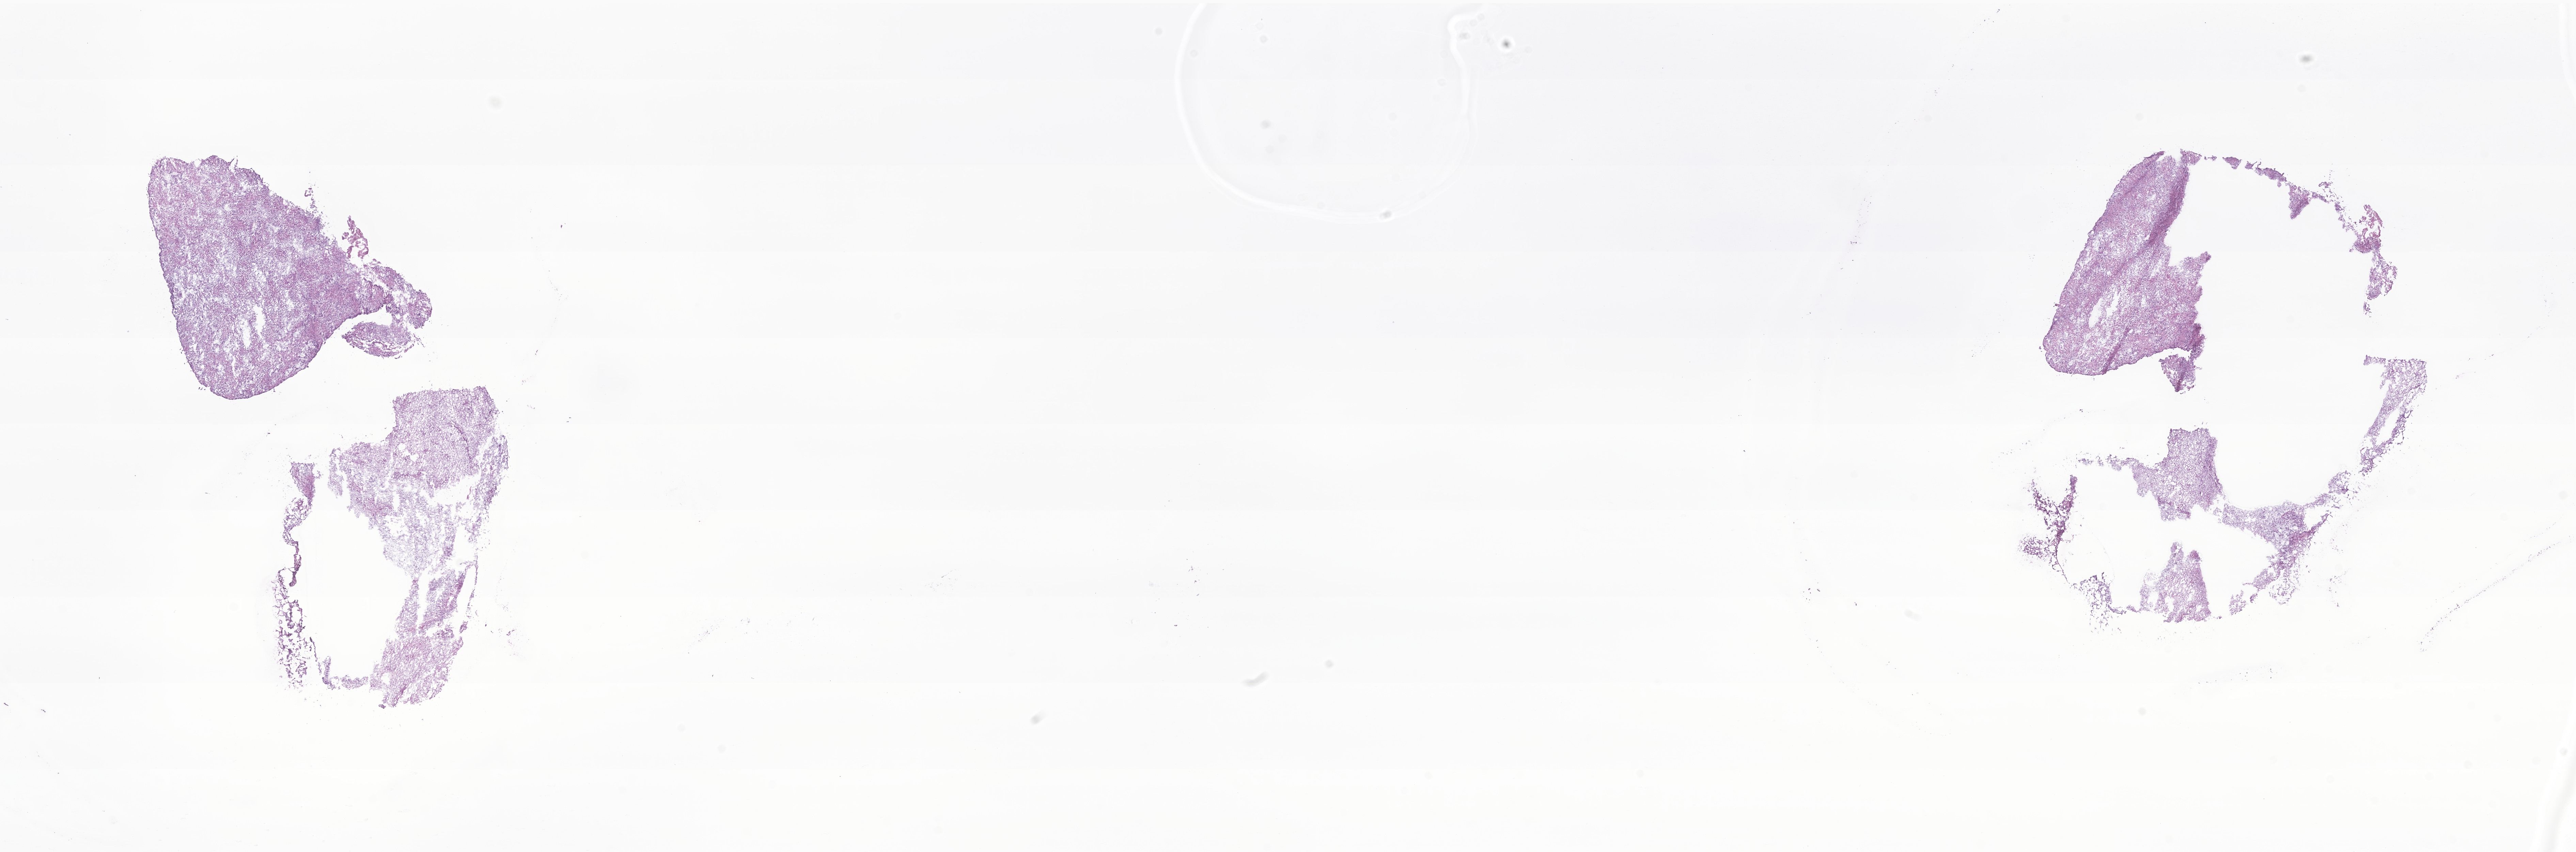
Hematoxylin and eosin (H&E) whole-slide image of tumor tissue from the cerebellum — whole scanned area (about 31.9 x 10.5 mm) shown as a low-resolution overview, frozen section (OCT-embedded). Patient female; age 704 days.
- diagnosis: Pilocytic astrocytoma